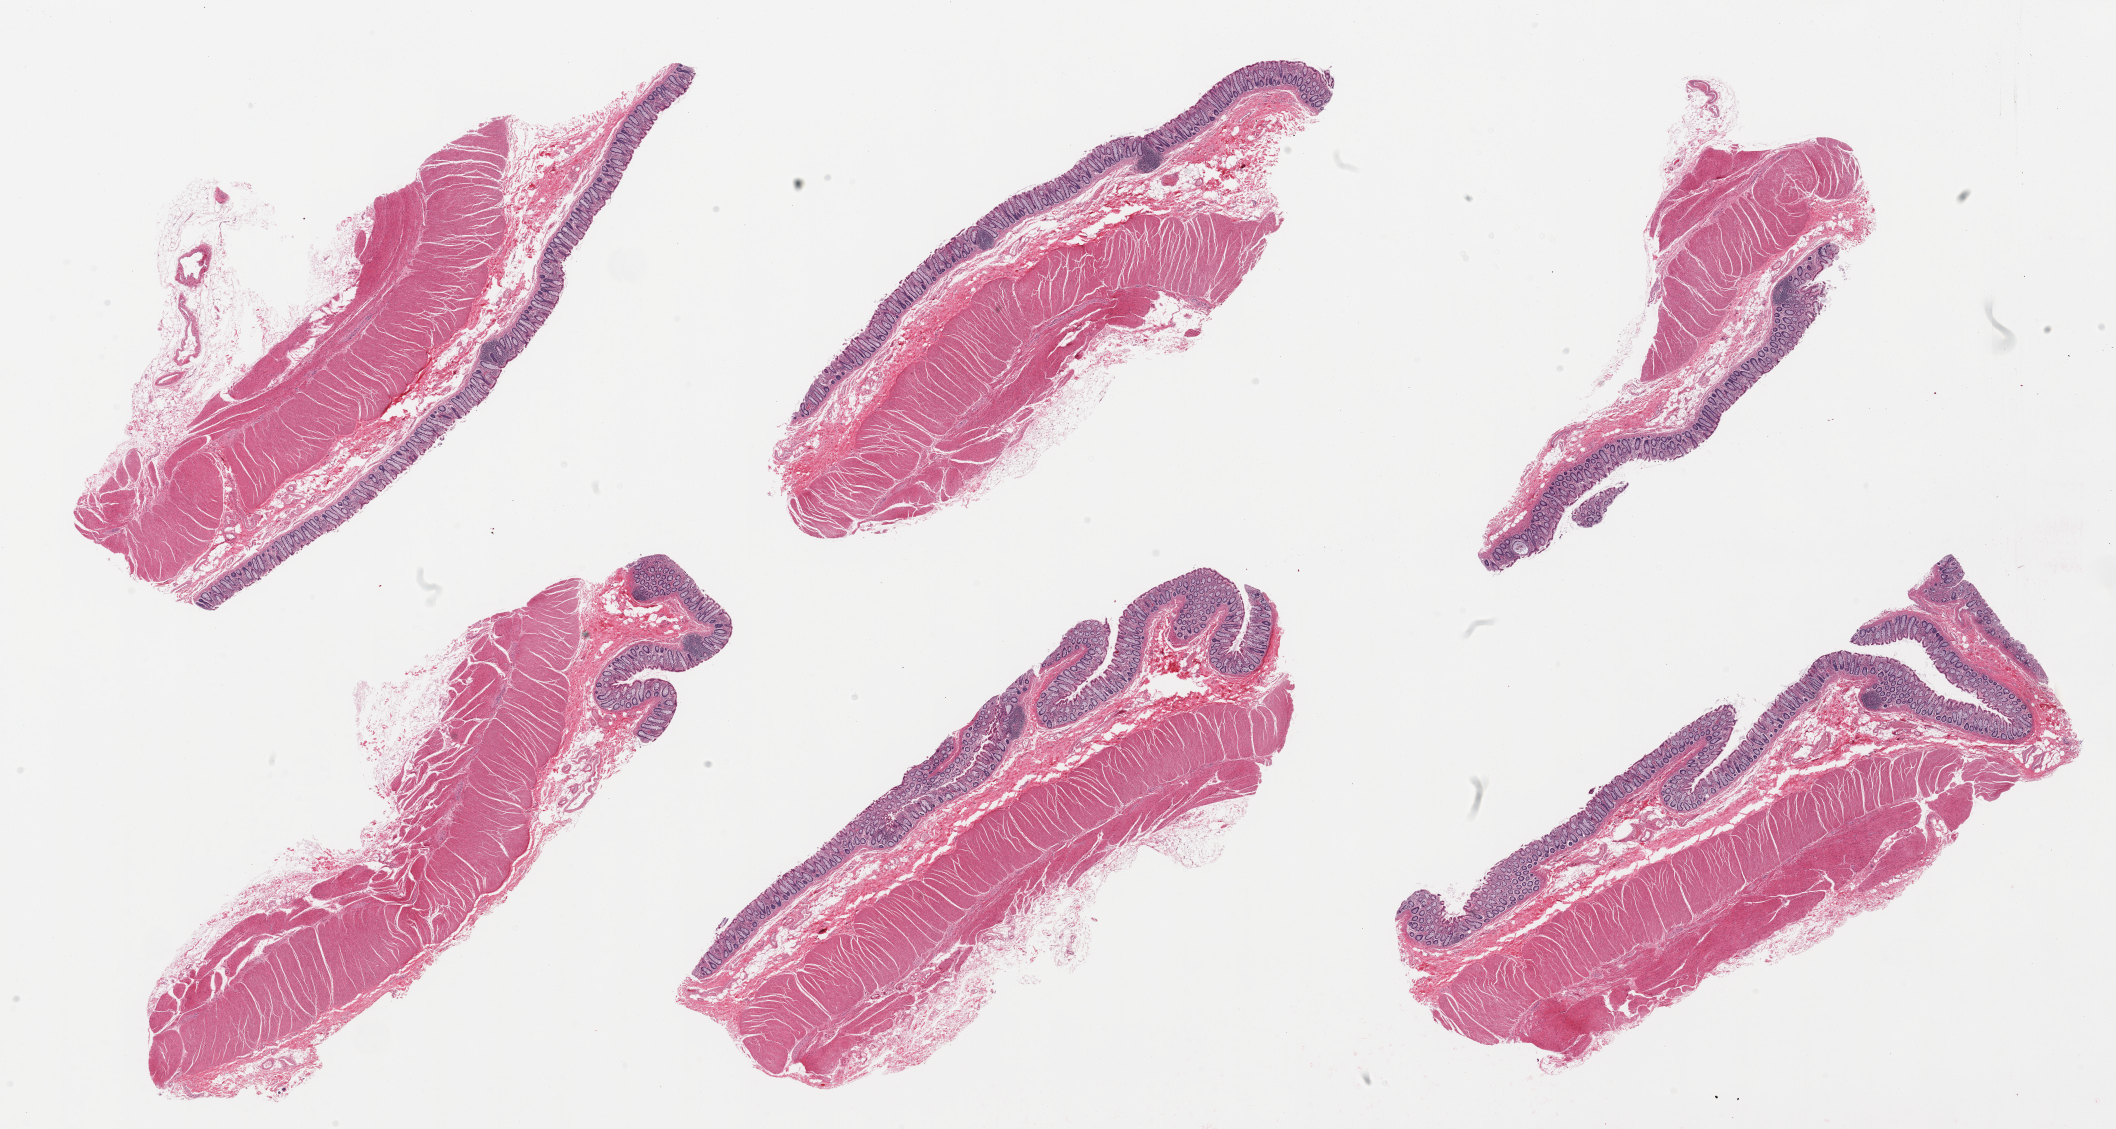
Digitized haematoxylin and eosin-stained section — whole scanned area (about 33.5 x 17.9 mm, acquisition: 20x scan) shown as a low-resolution overview, PAXgene-fixed paraffin-embedded (PFPE) section, target tissue: ileum, tissue donor sample. Donor sex: male.
Review note (as recorded): 6 pieces, colinic mucosa, only trace target lymphoid aggregates.